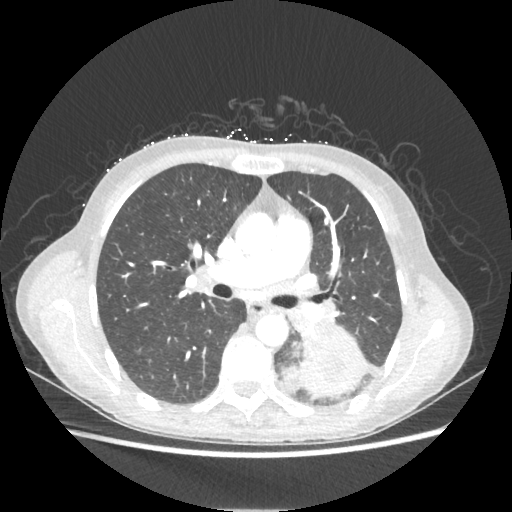
Chest CT, one axial slice; slice 129 of 221 in the series (ordered by position); reconstruction kernel STANDARD; lung window (W 1500 / L -600 HU); 1.25 mm slice thickness; 512 × 512 image matrix. Patient: female, 53 years. Case-level facts recorded for this patient, not image findings: clinical TNM (as recorded): T3 N0 M0.
Annotated regions visible in this slice (rectangle marked by the reading radiologist):
- lung tumour (recorded histology: adenocarcinoma): box from (x=276, y=331) to (x=370, y=400) px